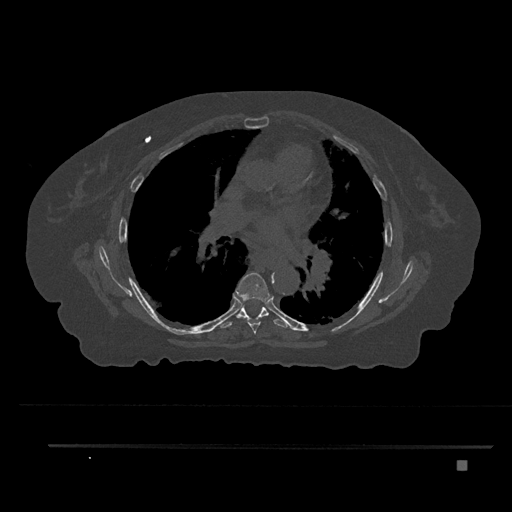
CT including the spine, one axial slice. Position 508 of 797 along the scan axis. Reconstruction kernel Br40s/3. 120 kVp. Bone window (W 1800 / L 400 HU). 512 × 512 image matrix. Female patient, age 76 years. Case-level facts recorded for this patient, not image findings: primary cancer: lung.
Outlined on this slice (semi-automatic segmentation, software-assisted and operator-edited):
- T6 vertebra: bounding box <234,273,270,334> (left, top, right, bottom; pixels)
- T7 vertebra: <219,306,288,328>